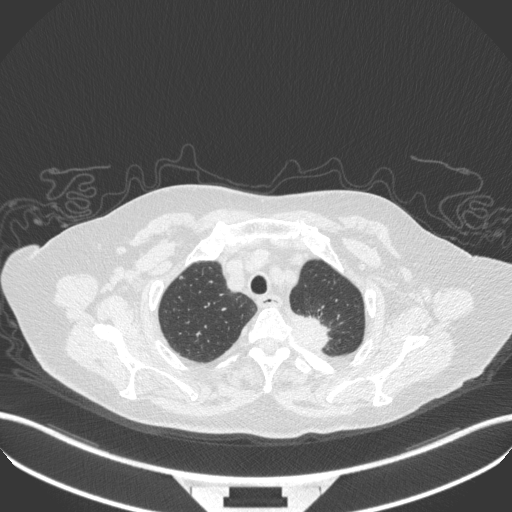
Chest CT, one axial slice. Slice 294 of 353 in the series (ordered by position). 100 kVp. Lung window (W 1500 / L -600 HU). 1 mm slice thickness. 512 × 512 image matrix. Female patient, age 81 years. Case-level facts recorded for this patient, not image findings: clinical TNM (as recorded): T2a N0 M0.
Annotated regions visible in this slice (bounding box drawn by a radiologist):
- lung tumour (recorded histology: adenocarcinoma): bounding box (x1, y1, x2, y2) in pixels: (284, 310, 332, 357)